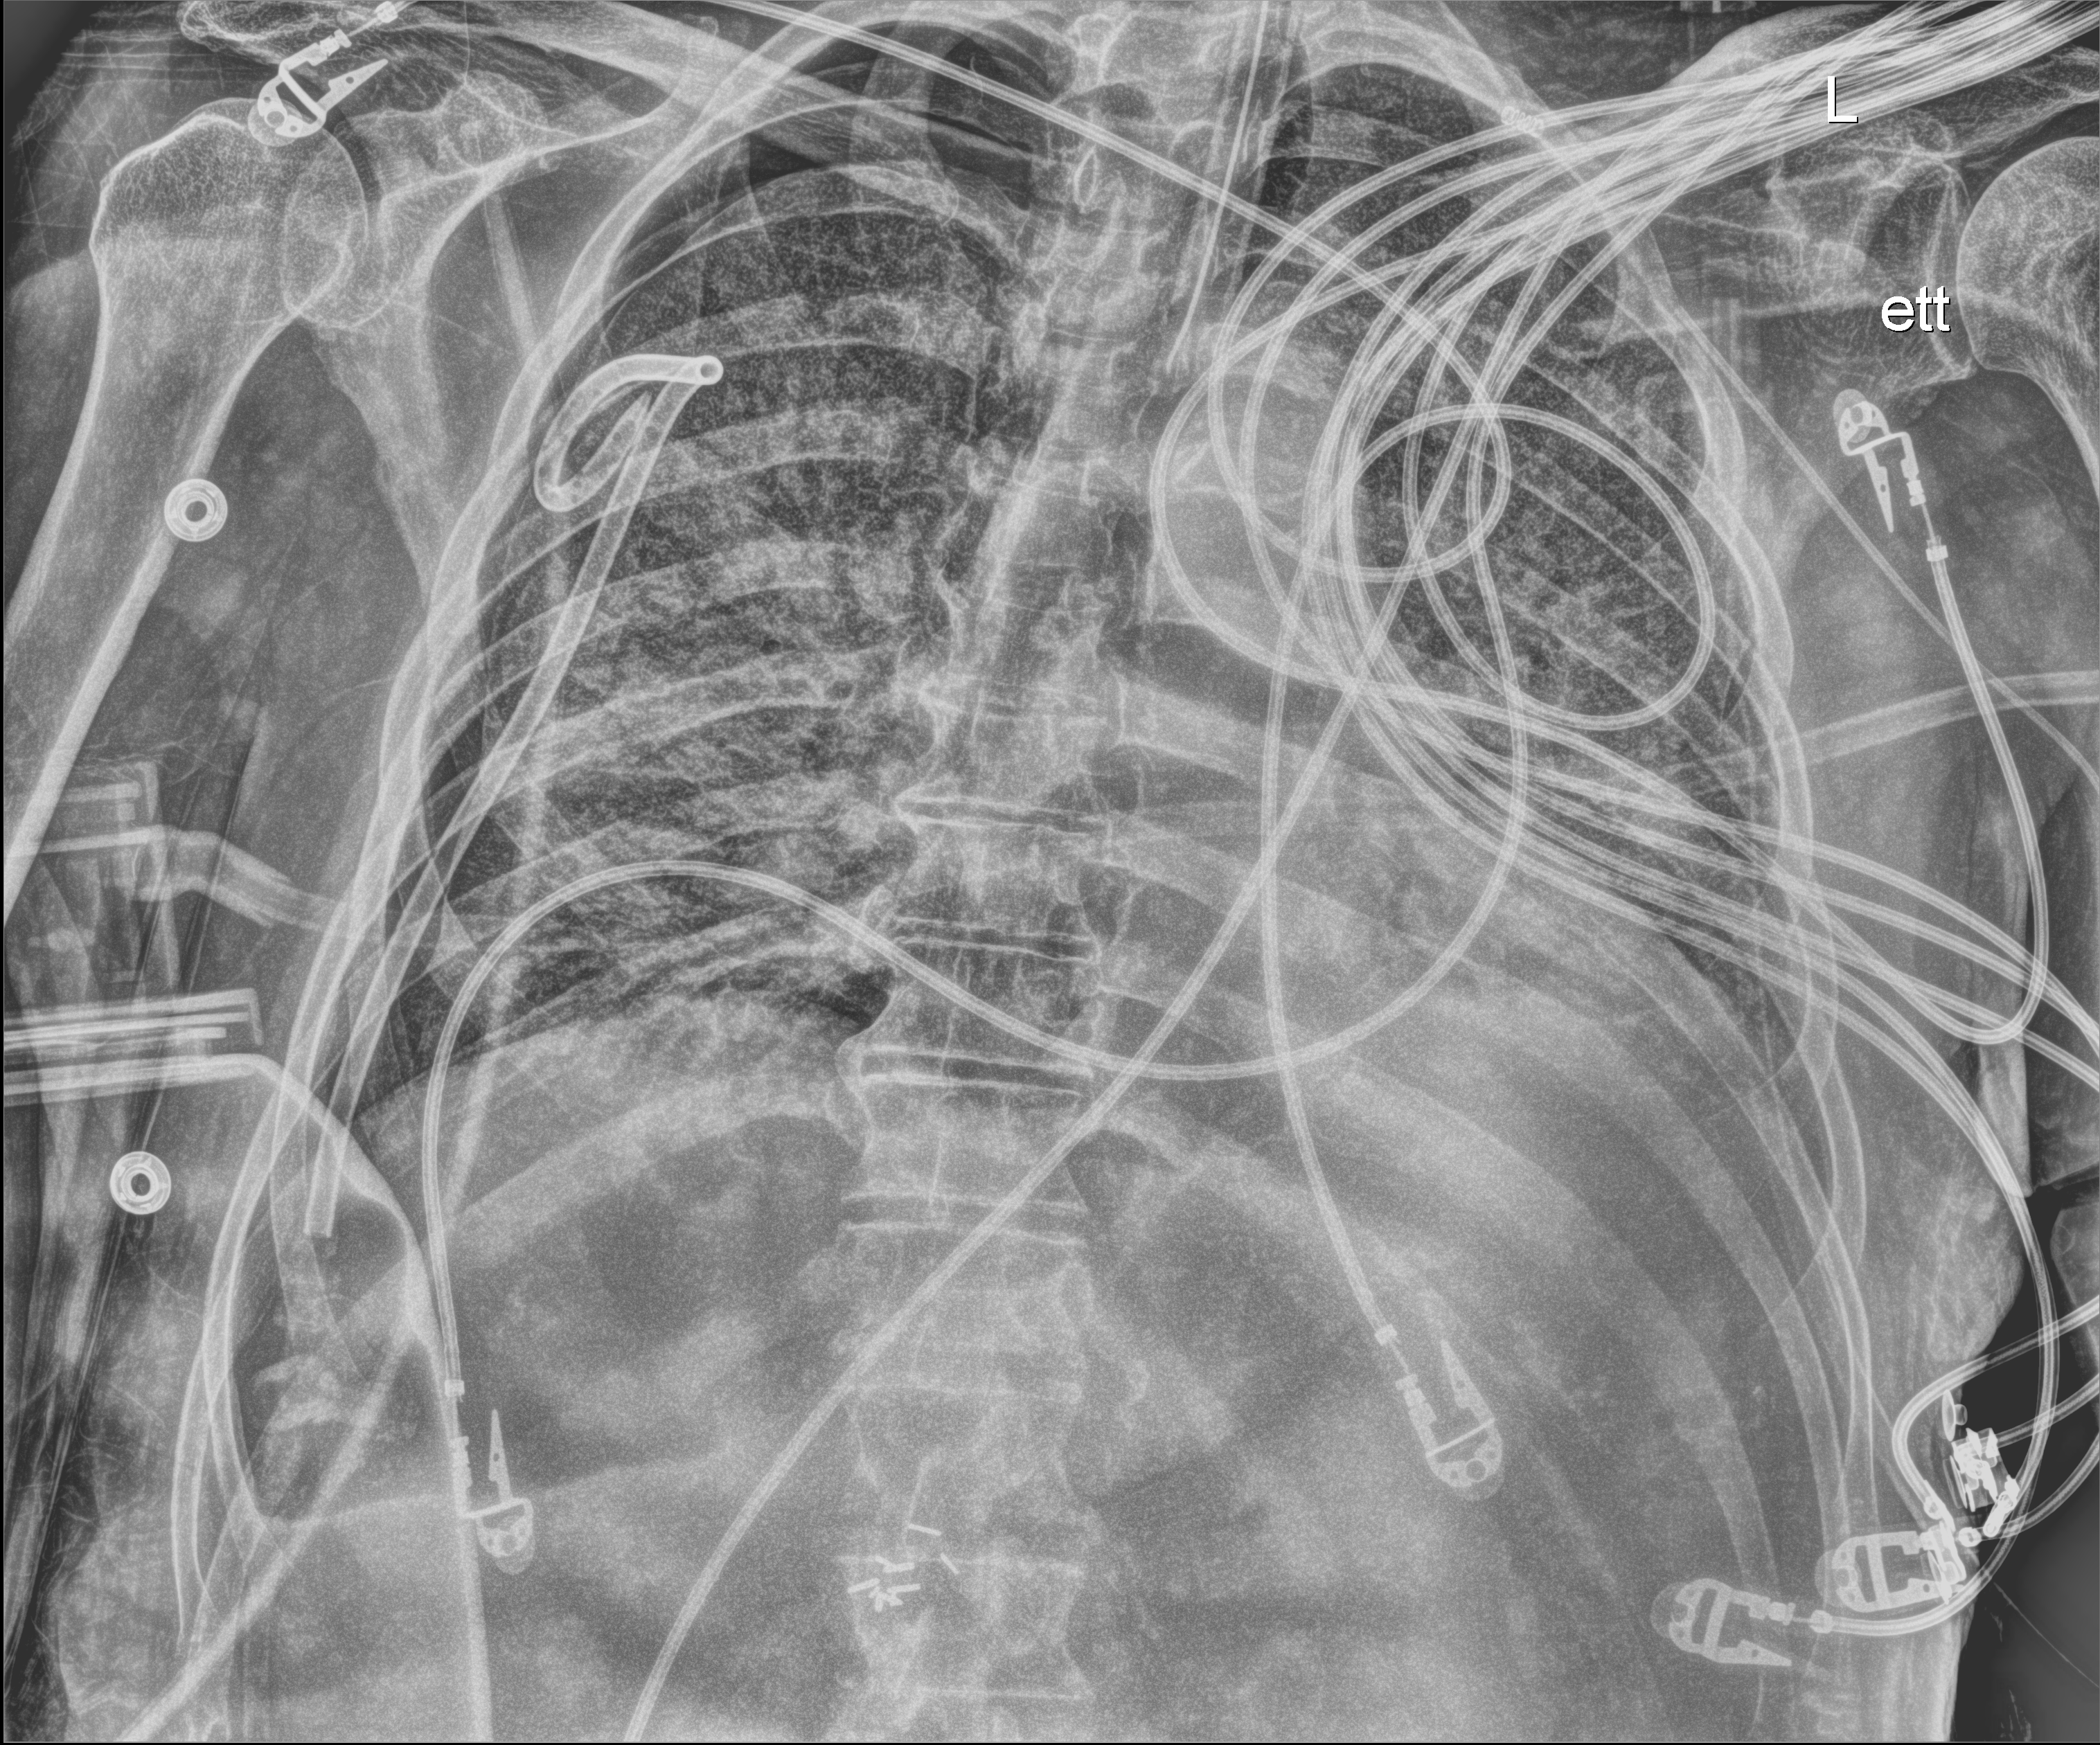
Chest X-ray (portable). Male patient hospitalised with COVID-19, age 75–90 years.
From the hospital-stay record, not from the radiograph (when in the stay this image was taken is not recorded):
- admitted to intensive care during this hospital stay: yes